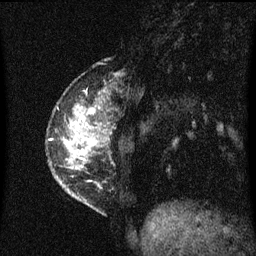
Breast MRI (dynamic contrast-enhanced), one sagittal slice. Position 15 of 60 along the scan axis. Dynamic contrast-enhanced series, image 2 of 3 at this slice position (ordered by acquisition). 1.5 T. TE 4.2 ms, TR 8.4 ms. 2 mm slice thickness. 256 × 256 image matrix. Female patient, age 34 years. From the clinical record (not read from this slice): setting: breast cancer imaged before/during neoadjuvant chemotherapy; receptor status: HR-positive, HER2-negative.
Outlined on this slice (semi-automatic segmentation, software-assisted and operator-edited):
- analysis volume of interest (the breast-tissue region the enhancement analysis was run in; not a lesion): bounding box (x1, y1, x2, y2) in pixels: (58, 102, 107, 207)
- tumour enhancement mask (voxels above the 70 % enhancement threshold inside the analysis volume of interest): (76, 110, 95, 127)